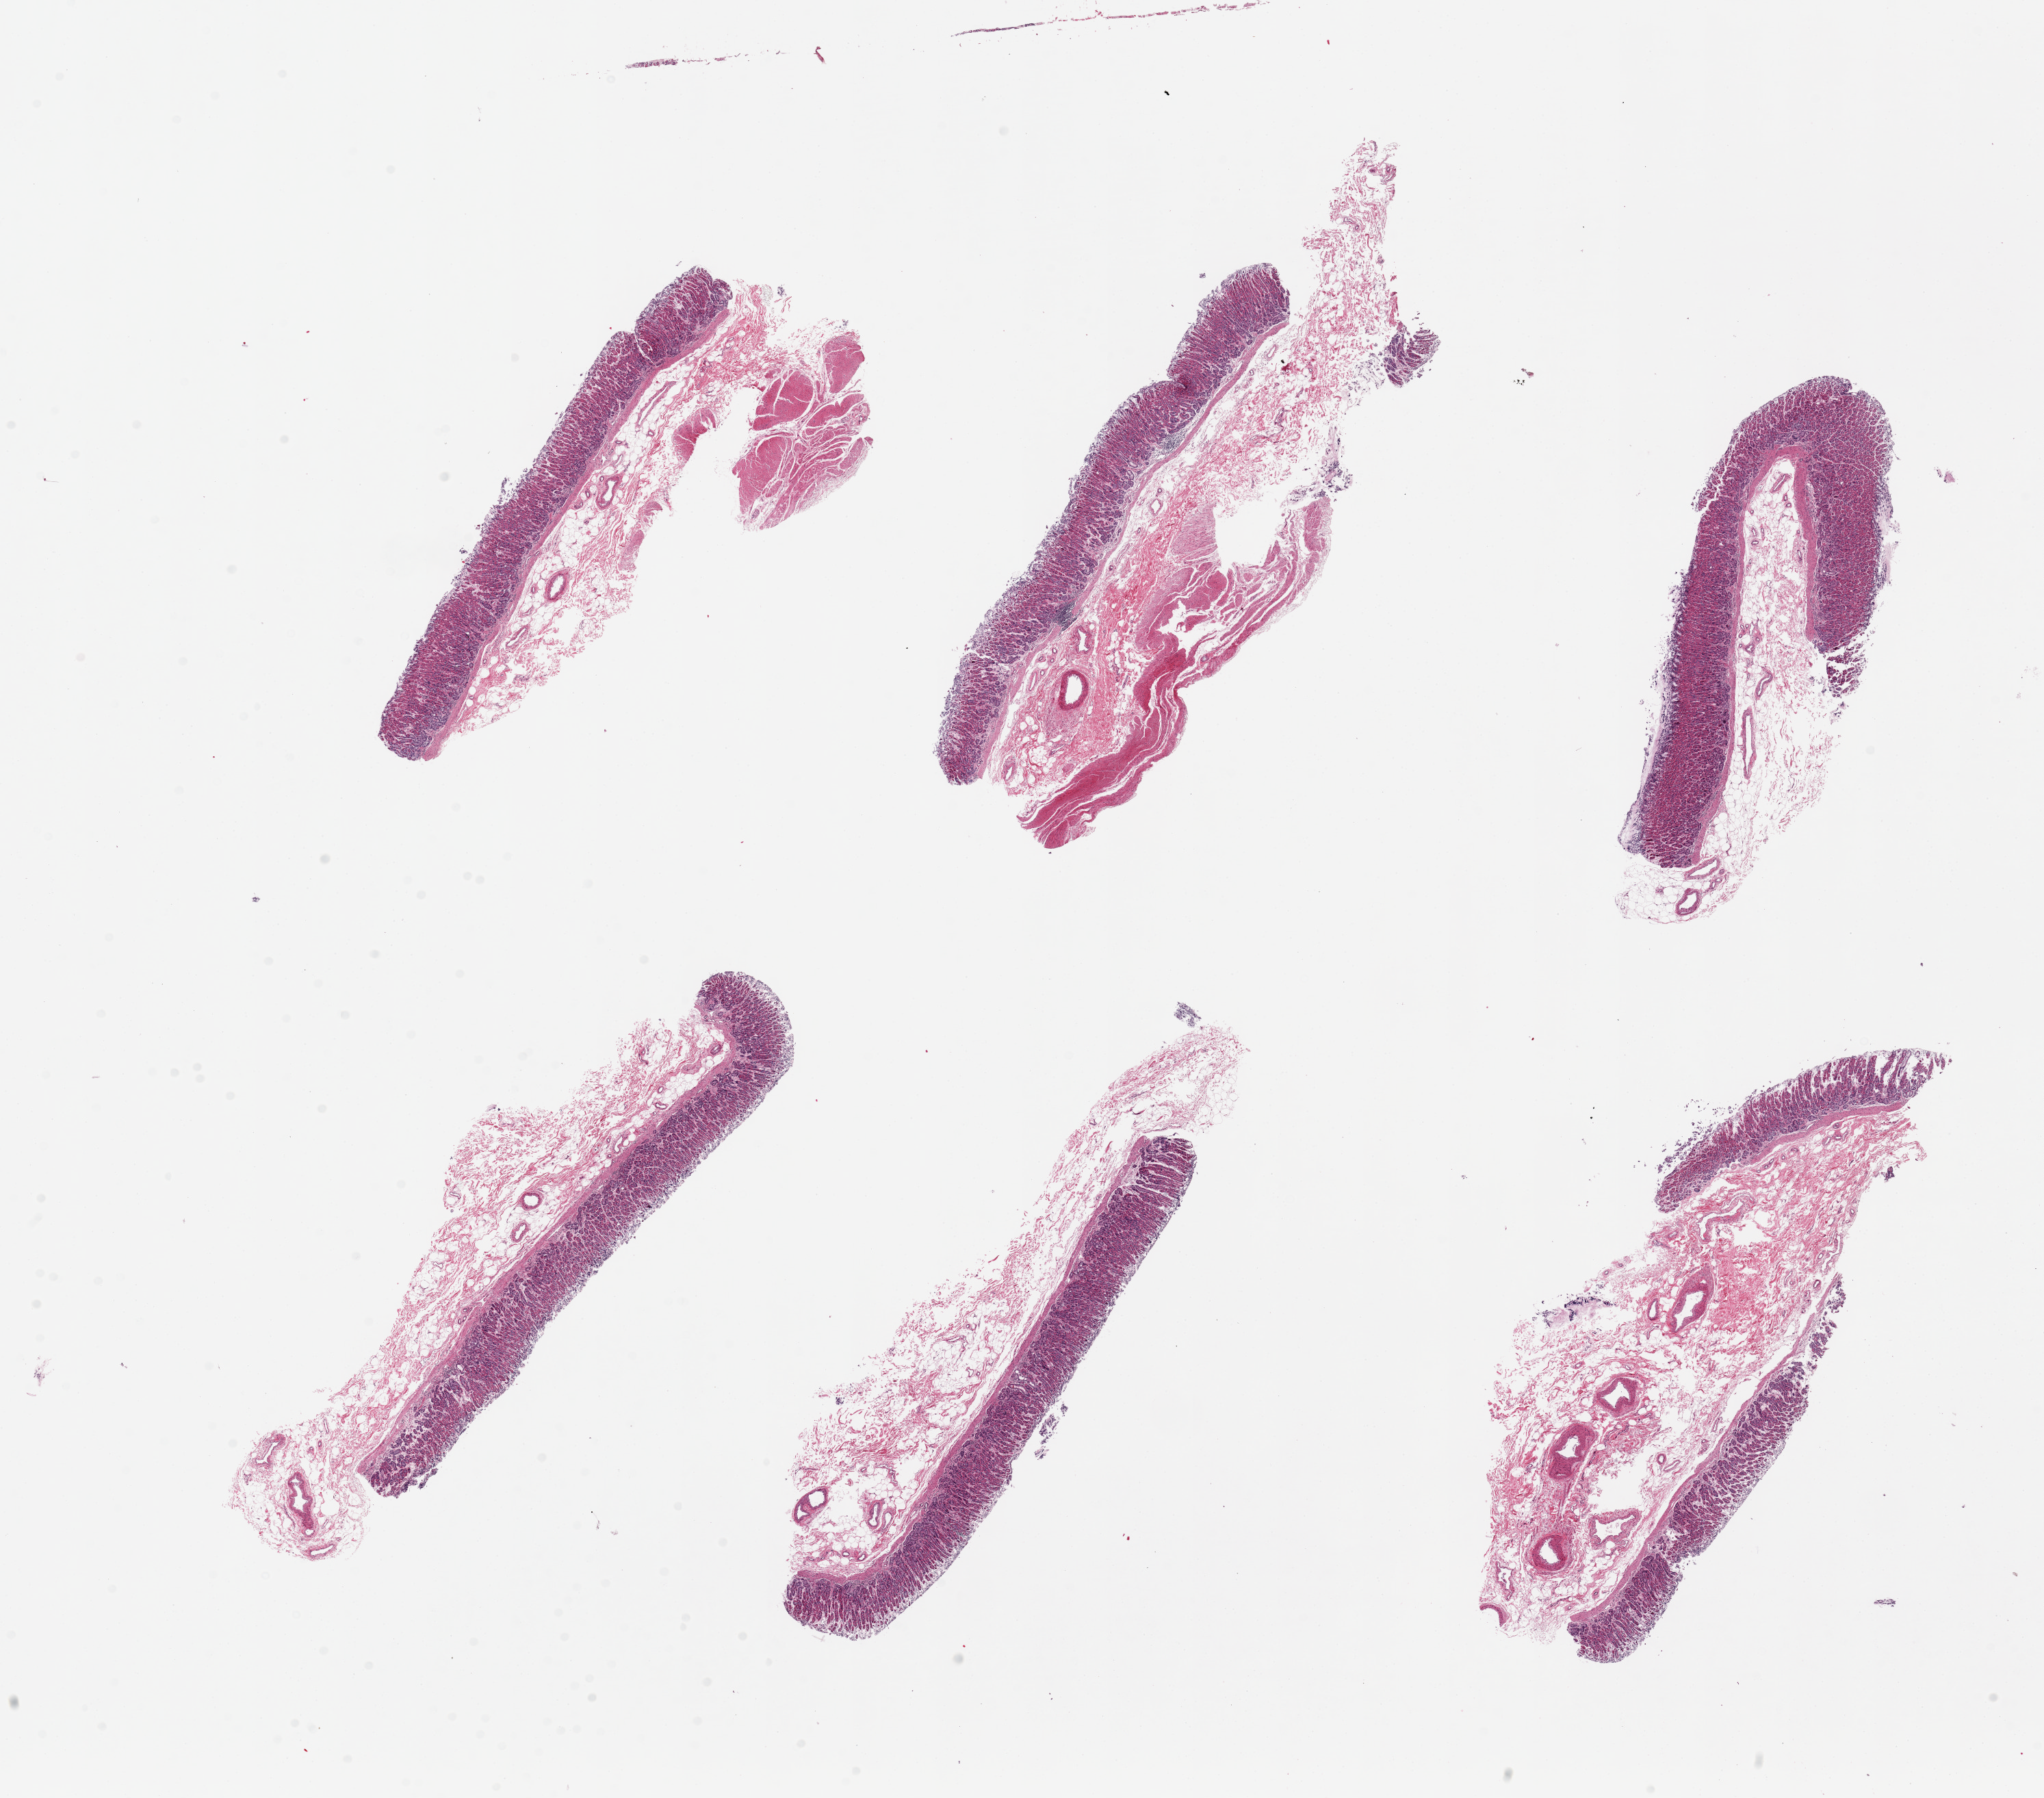
Whole-slide image, H&E stain — low-resolution overview of the scanned area, about 23.6 x 20.8 mm, PAXgene-fixed, paraffin-embedded tissue, section of stomach (target tissue), donor tissue sample. Male donor.
- pathologist's review note for this sample: 6 pieces, up to 9x3mm; foveolar (surface) glands autolyzed; only 1 of 6 has muscularis